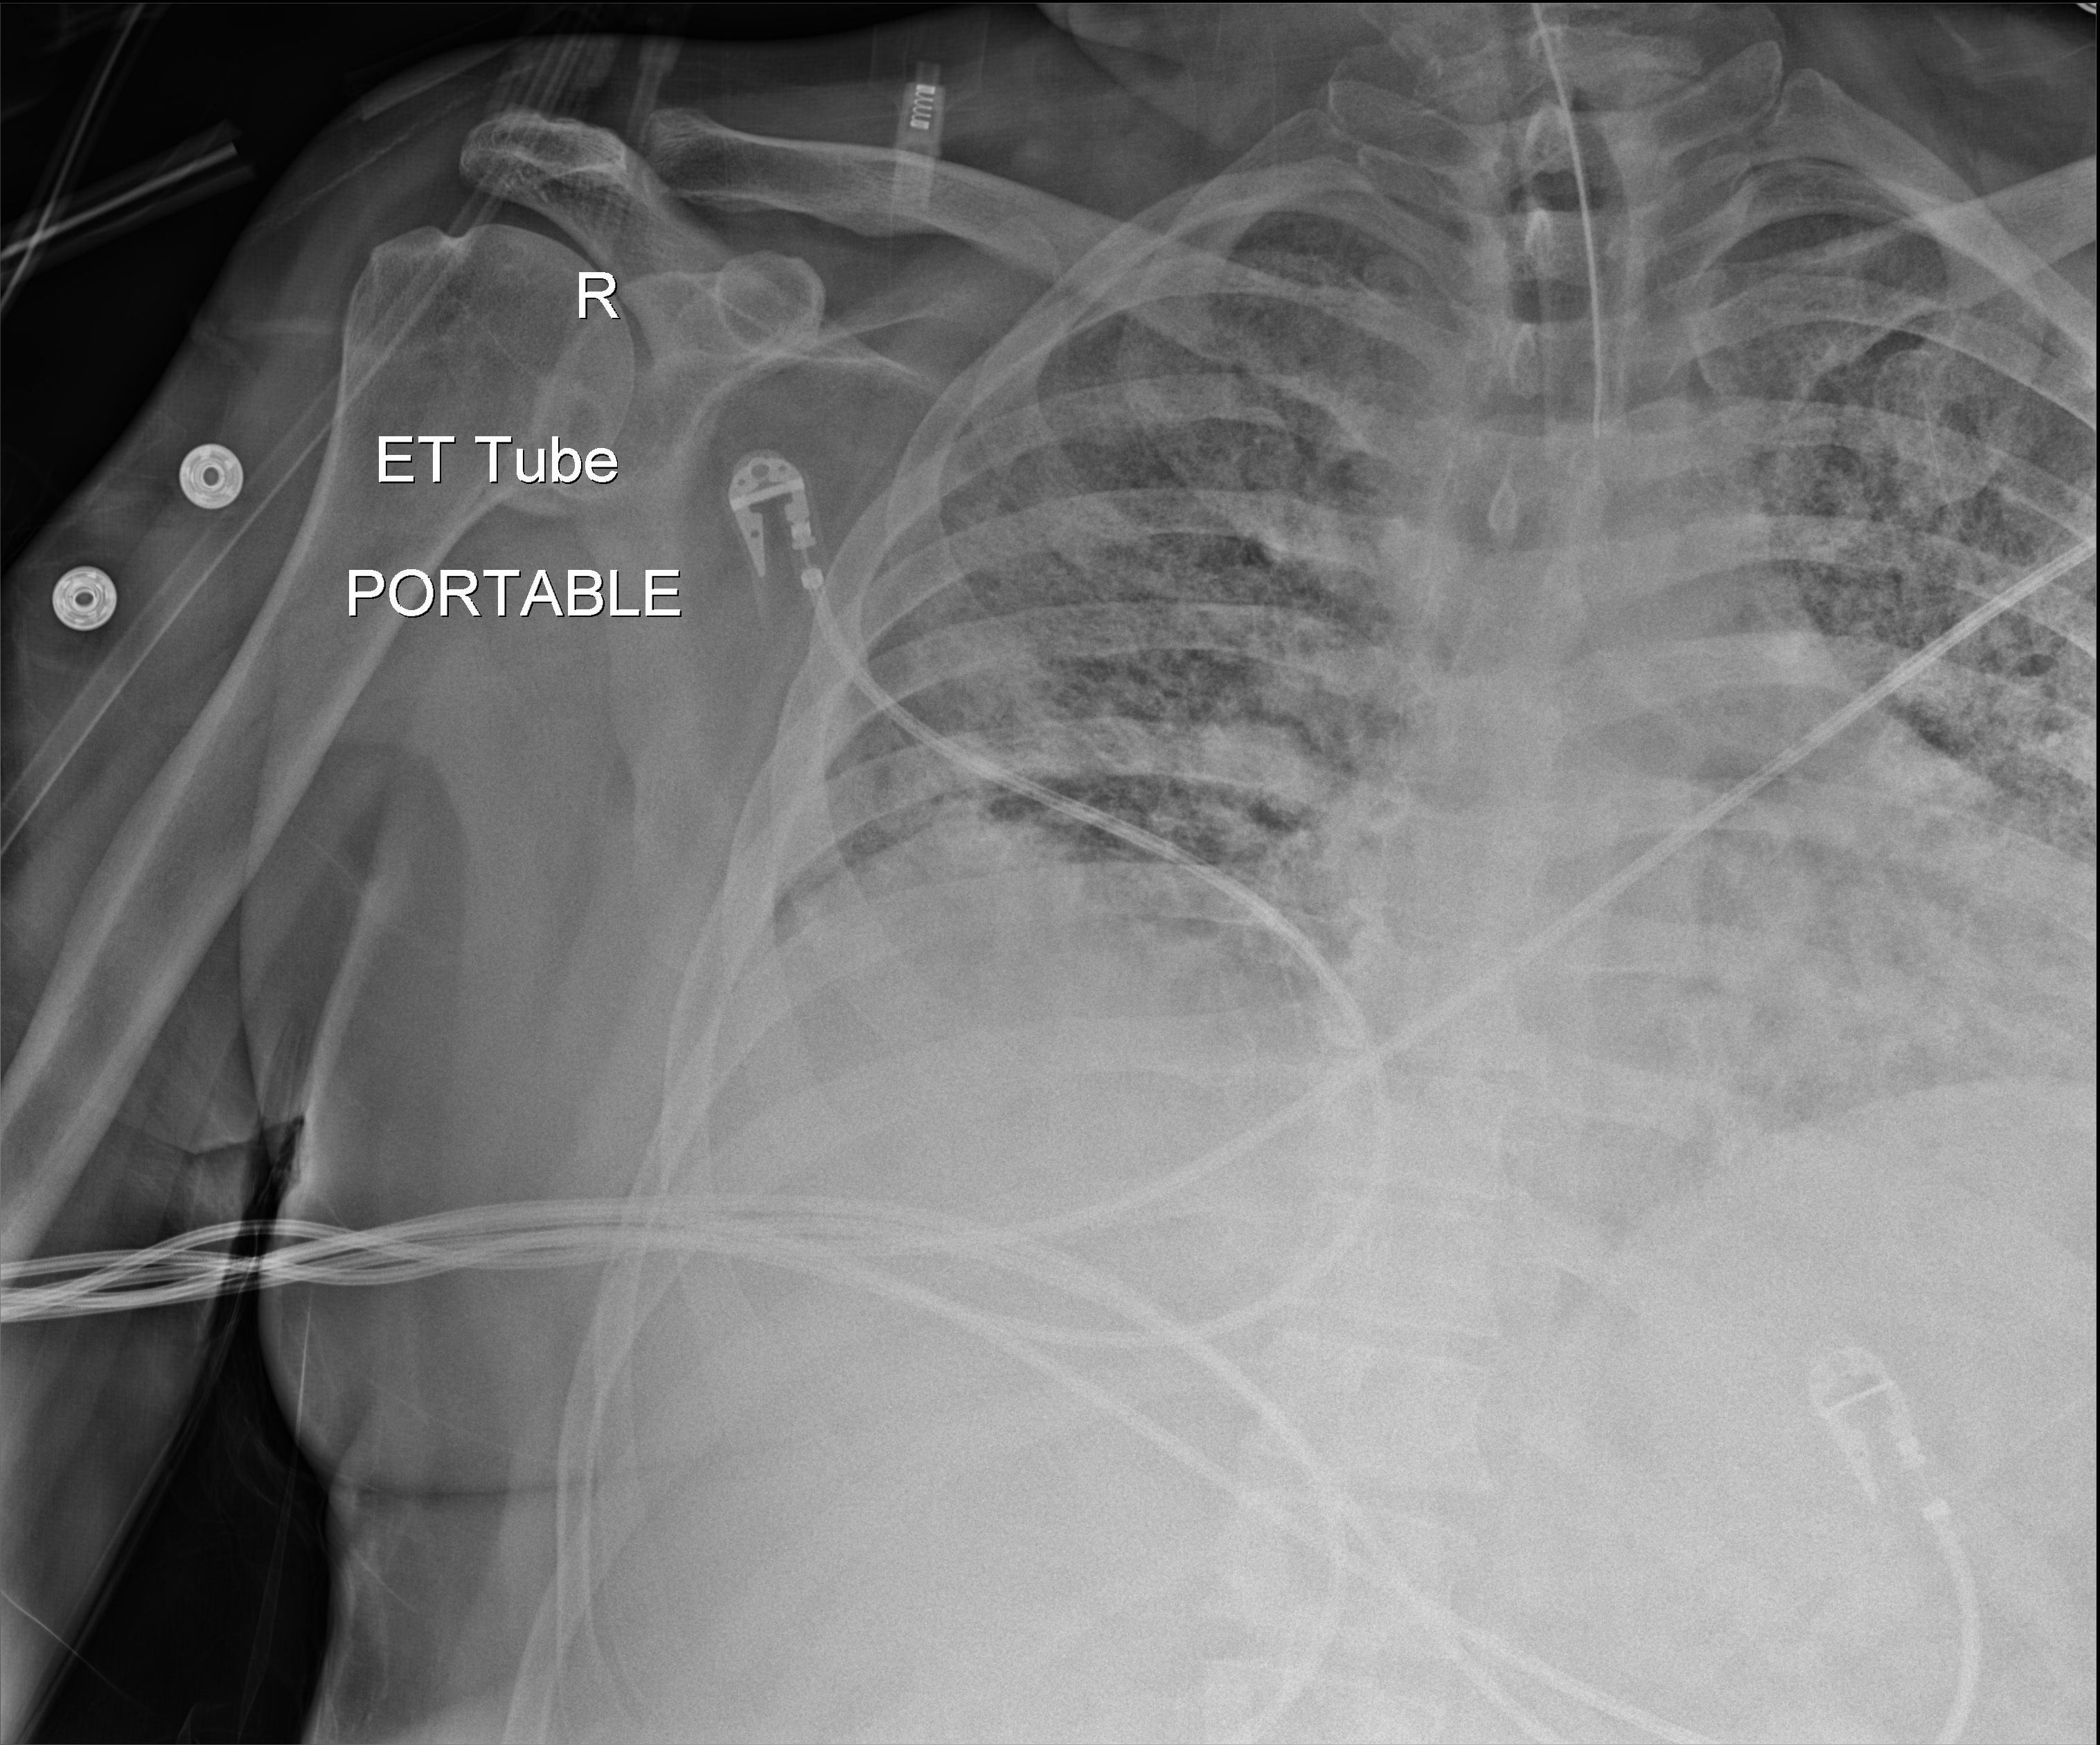
Chest X-ray; anteroposterior (AP) projection. Patient hospitalised with COVID-19; male, aged 18–59 years.
Hospital-stay facts (about this admission, not read from this image; timing relative to this image not recorded): other chronic lung disease (admission record): no.